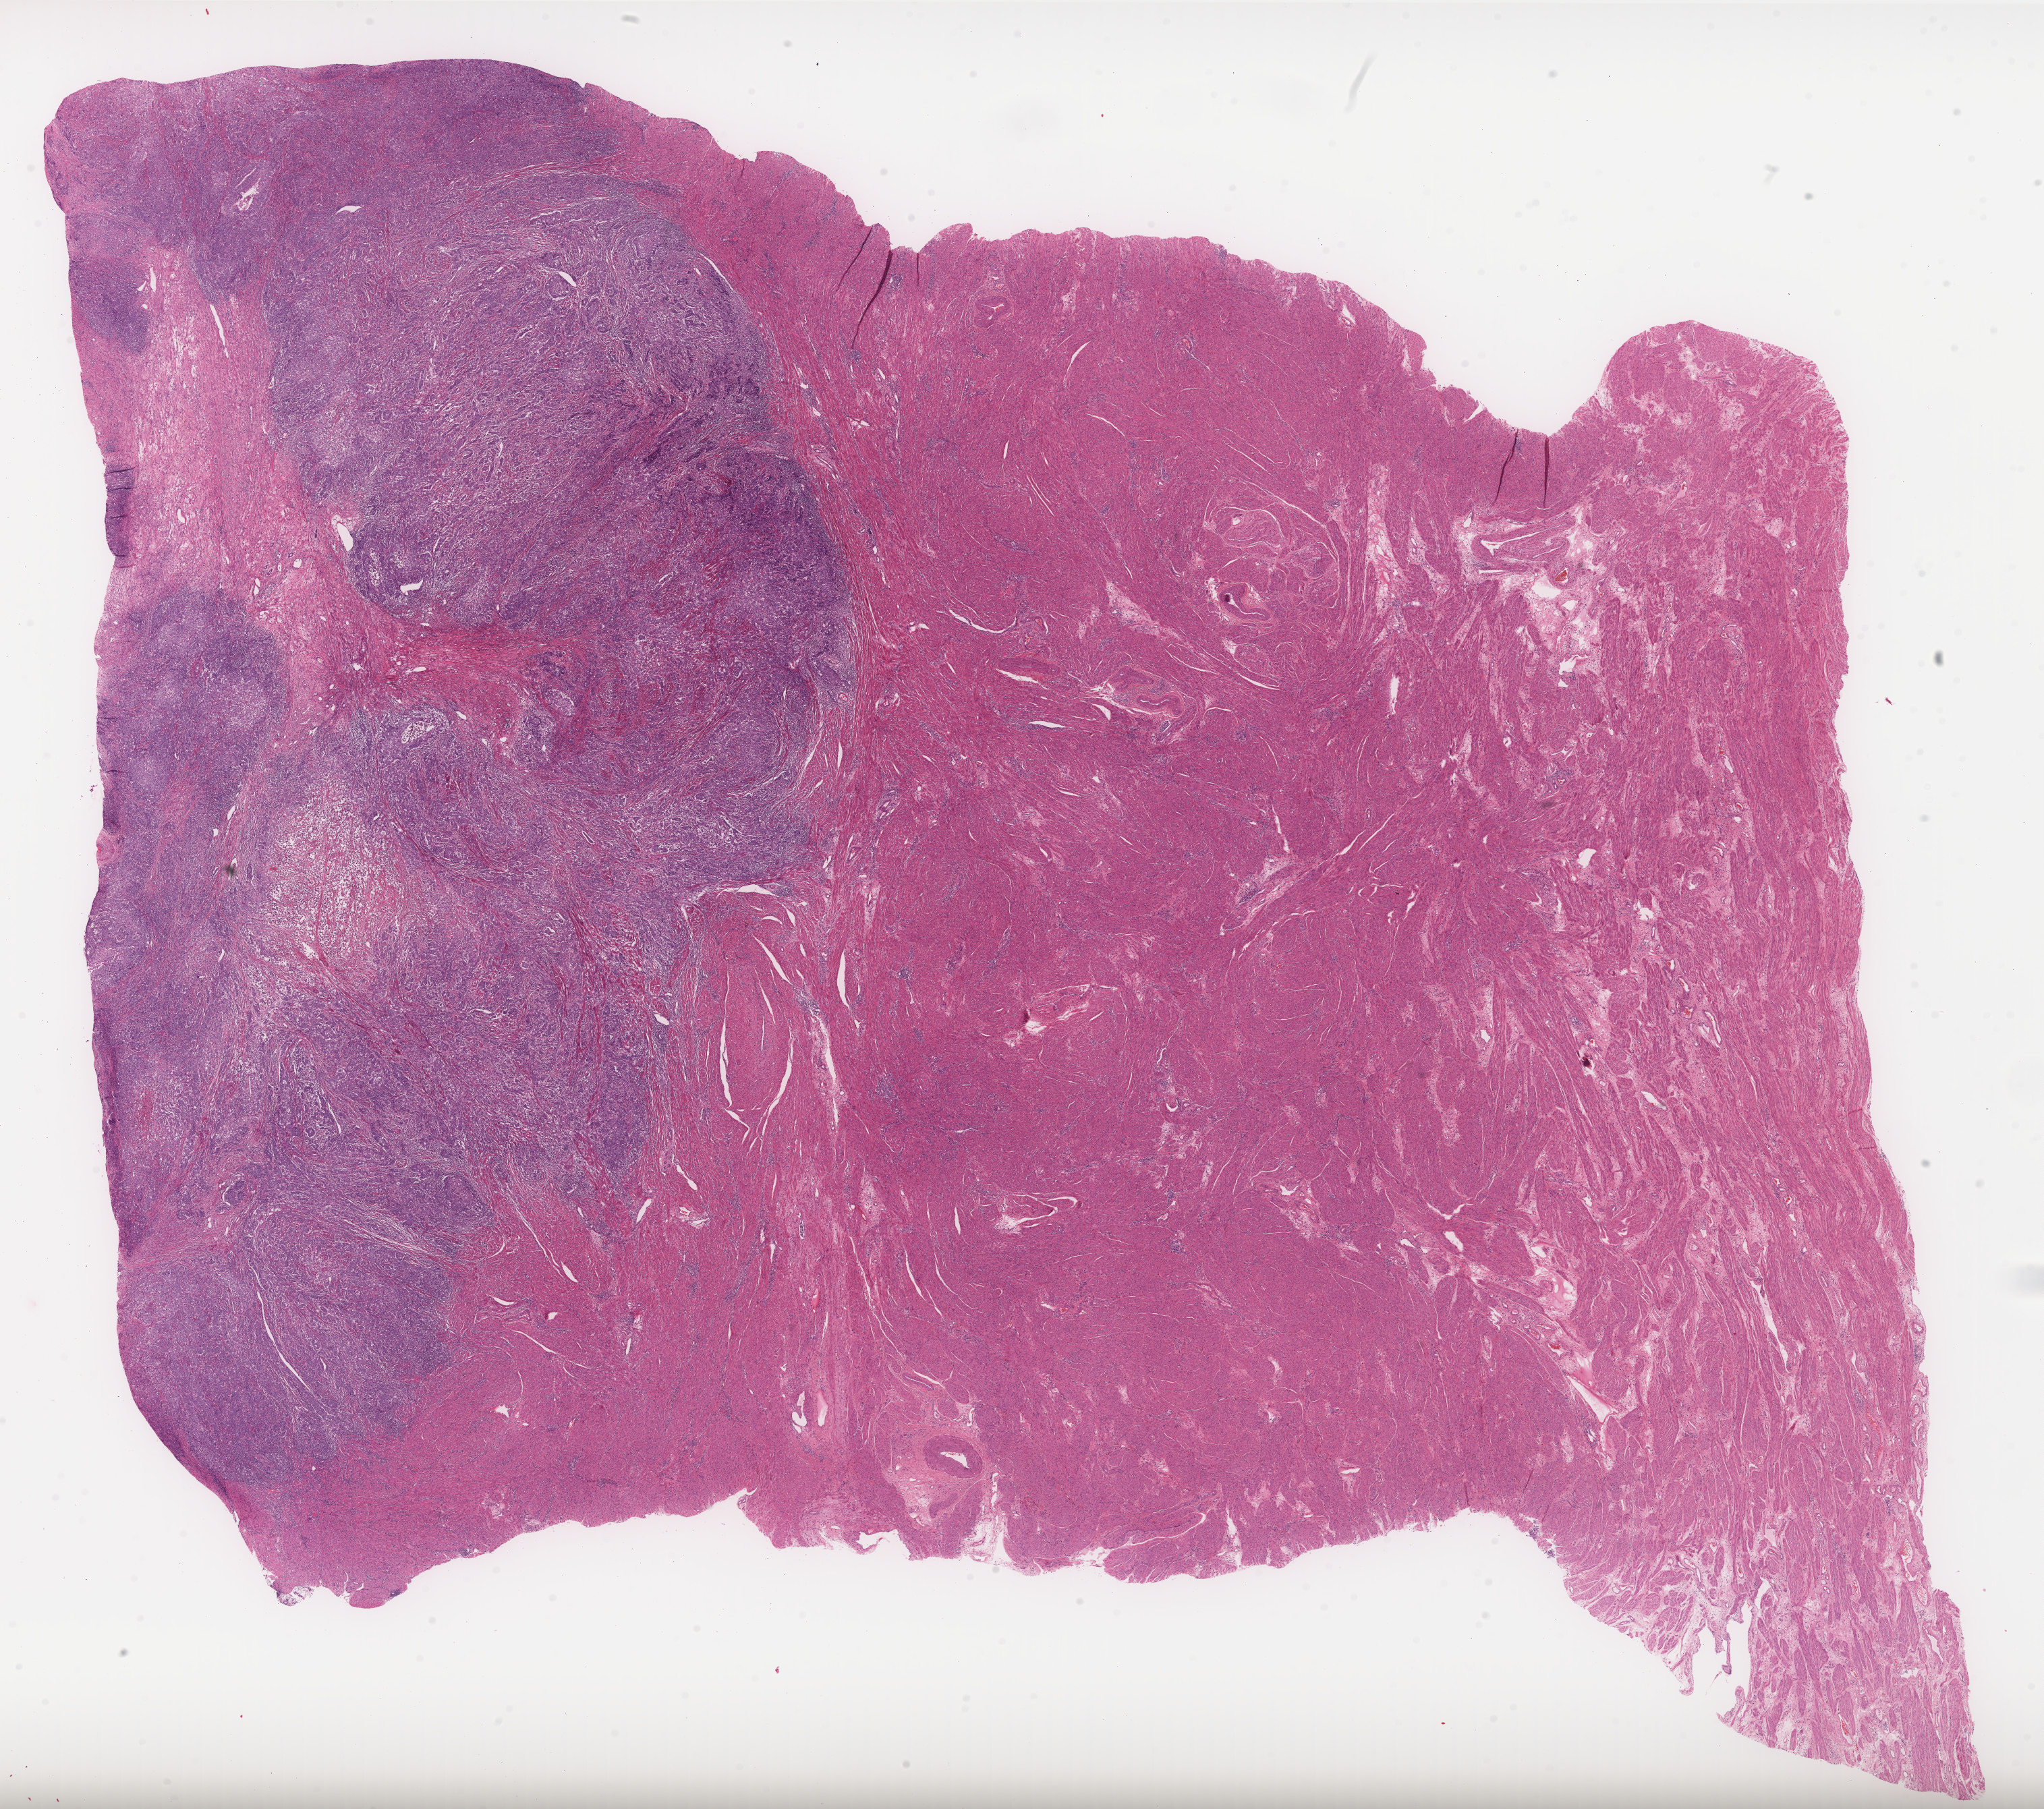
Whole-slide histology image, Hematoxylin and eosin (H&E) stained, a low-resolution overview of the entire scanned area, about 24.3 x 21.5 mm, FFPE section, primary tumour sample from the uterus. Female patient; age at initial diagnosis 65 years.
Pathologic diagnosis: Endometrioid adenocarcinoma, NOS (endometrium).